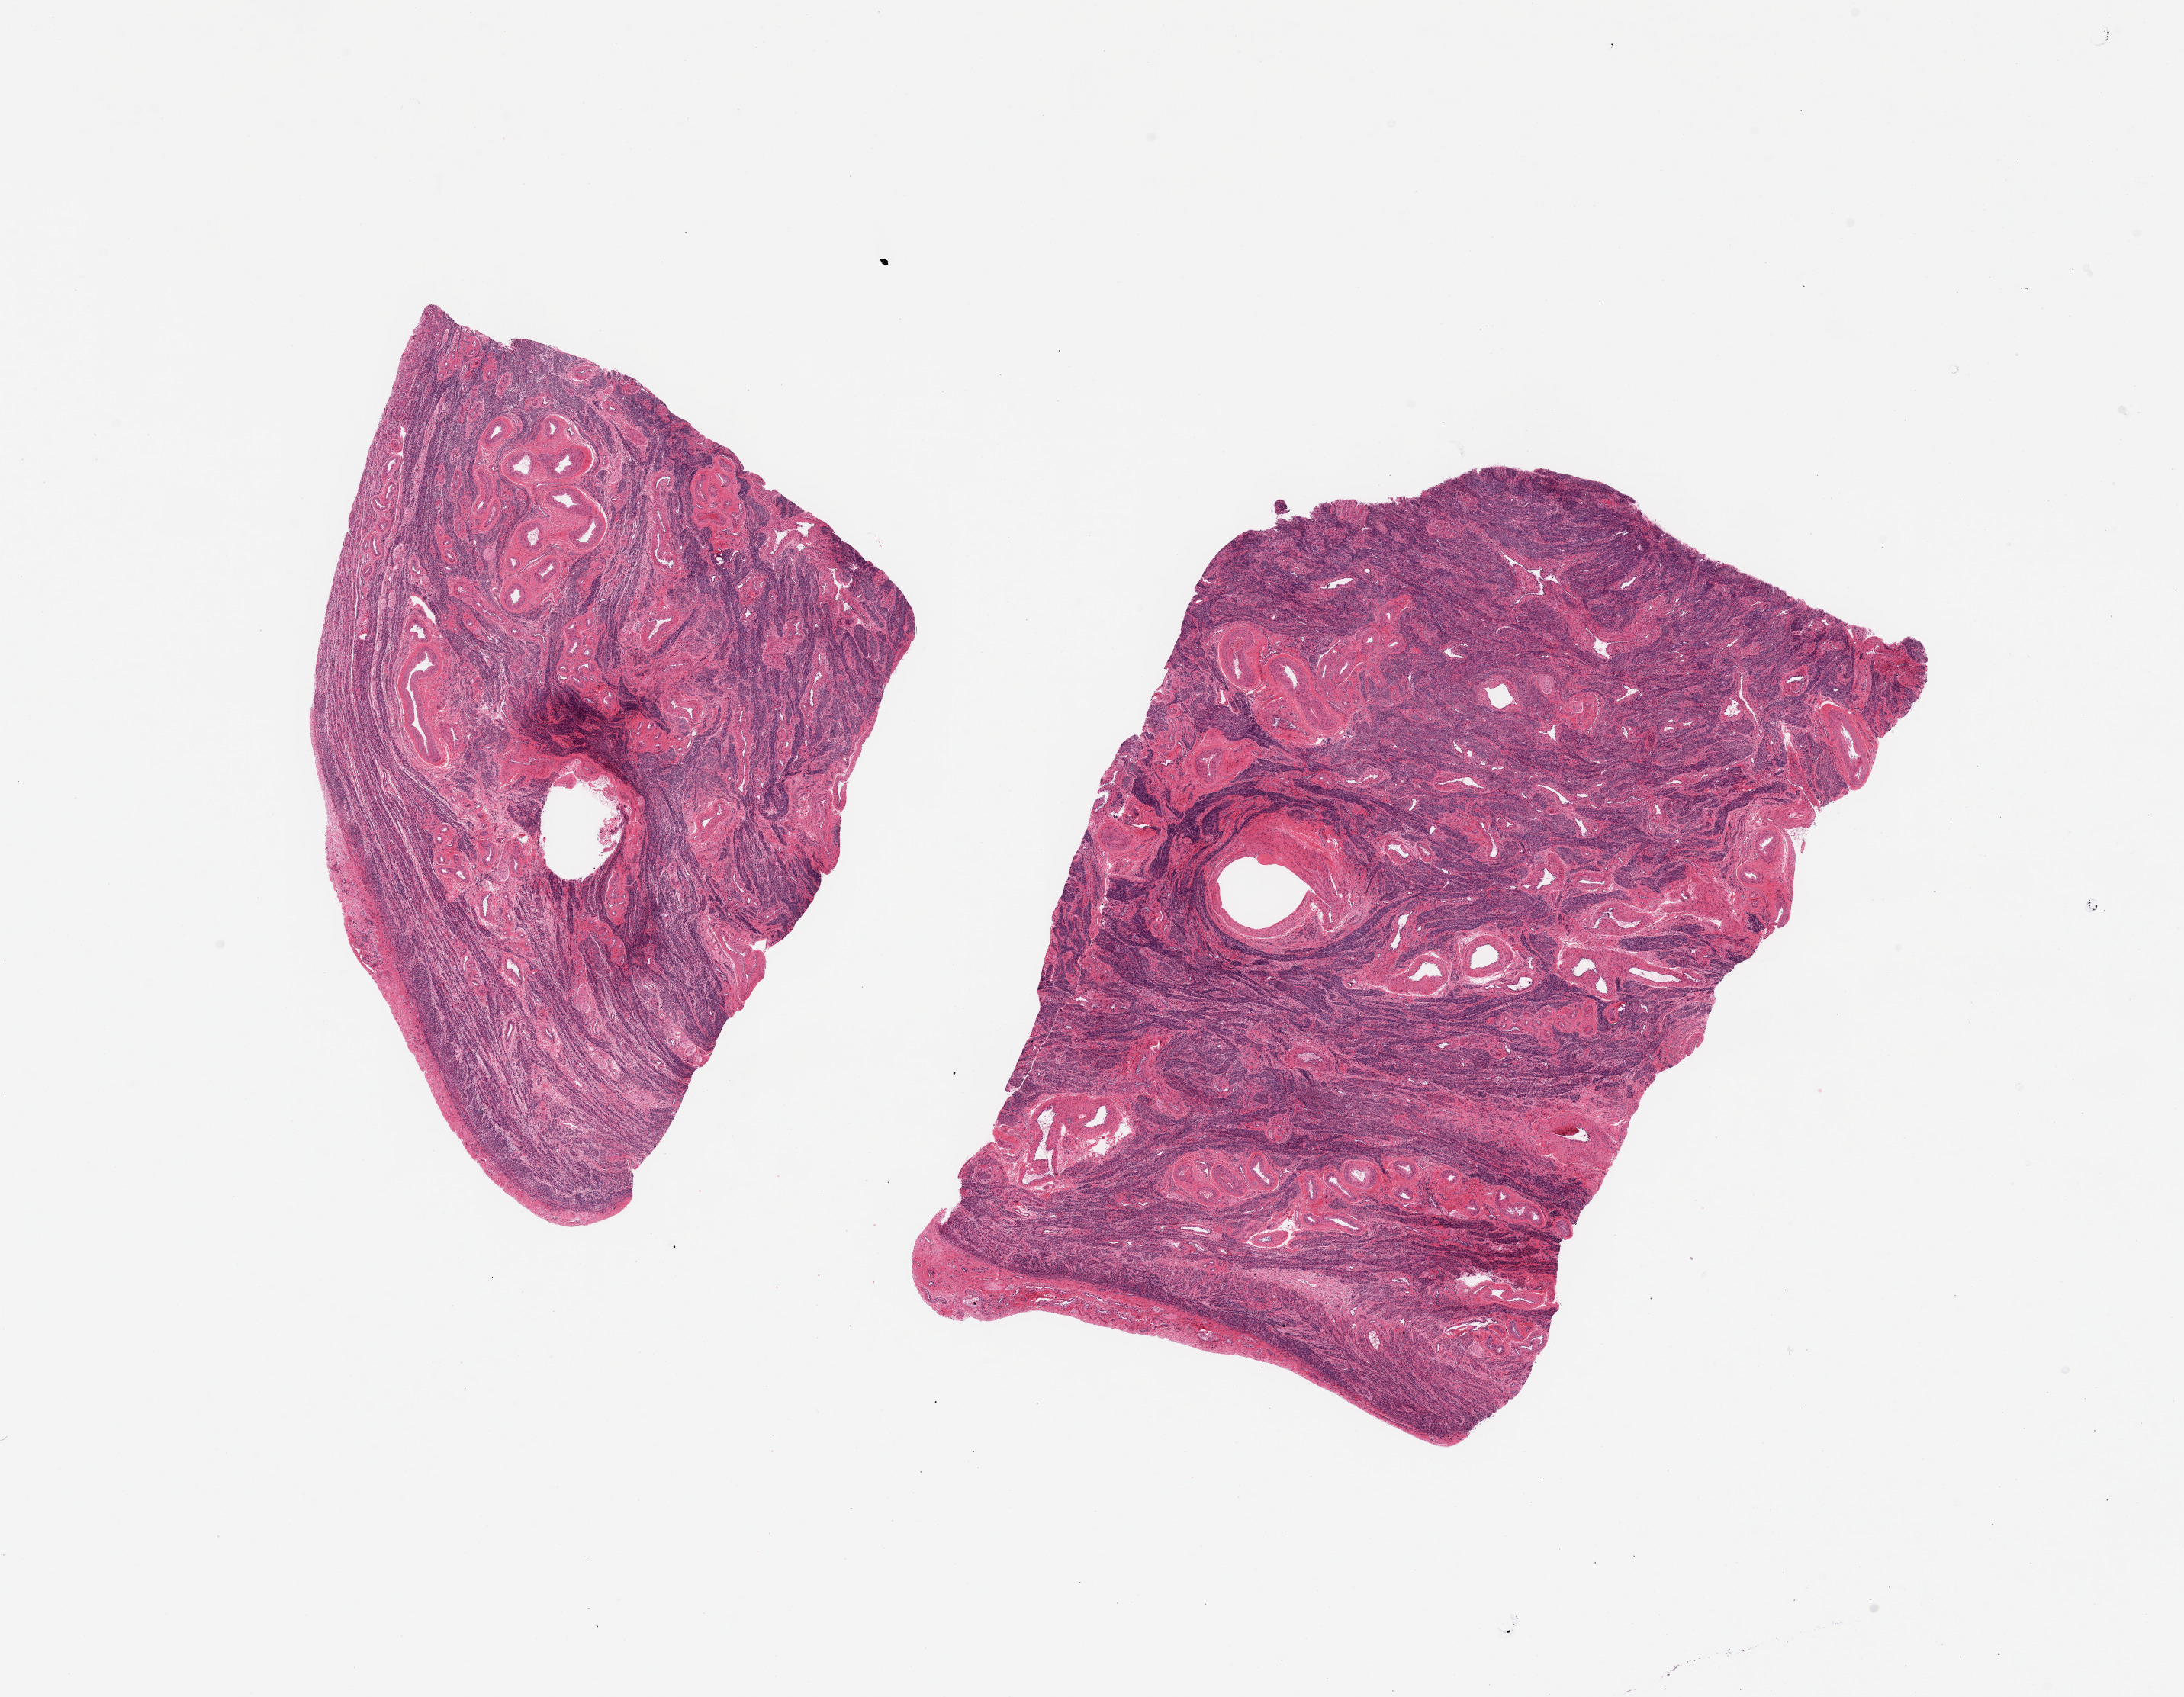
H&E whole-slide image — low-resolution overview of the scanned area, about 22.6 x 17.6 mm; PAXgene-fixed, paraffin-embedded tissue; section of uterus (target tissue); tissue donor sample. Donor: female.
- review note (as recorded): 2 pieces, myometrium only